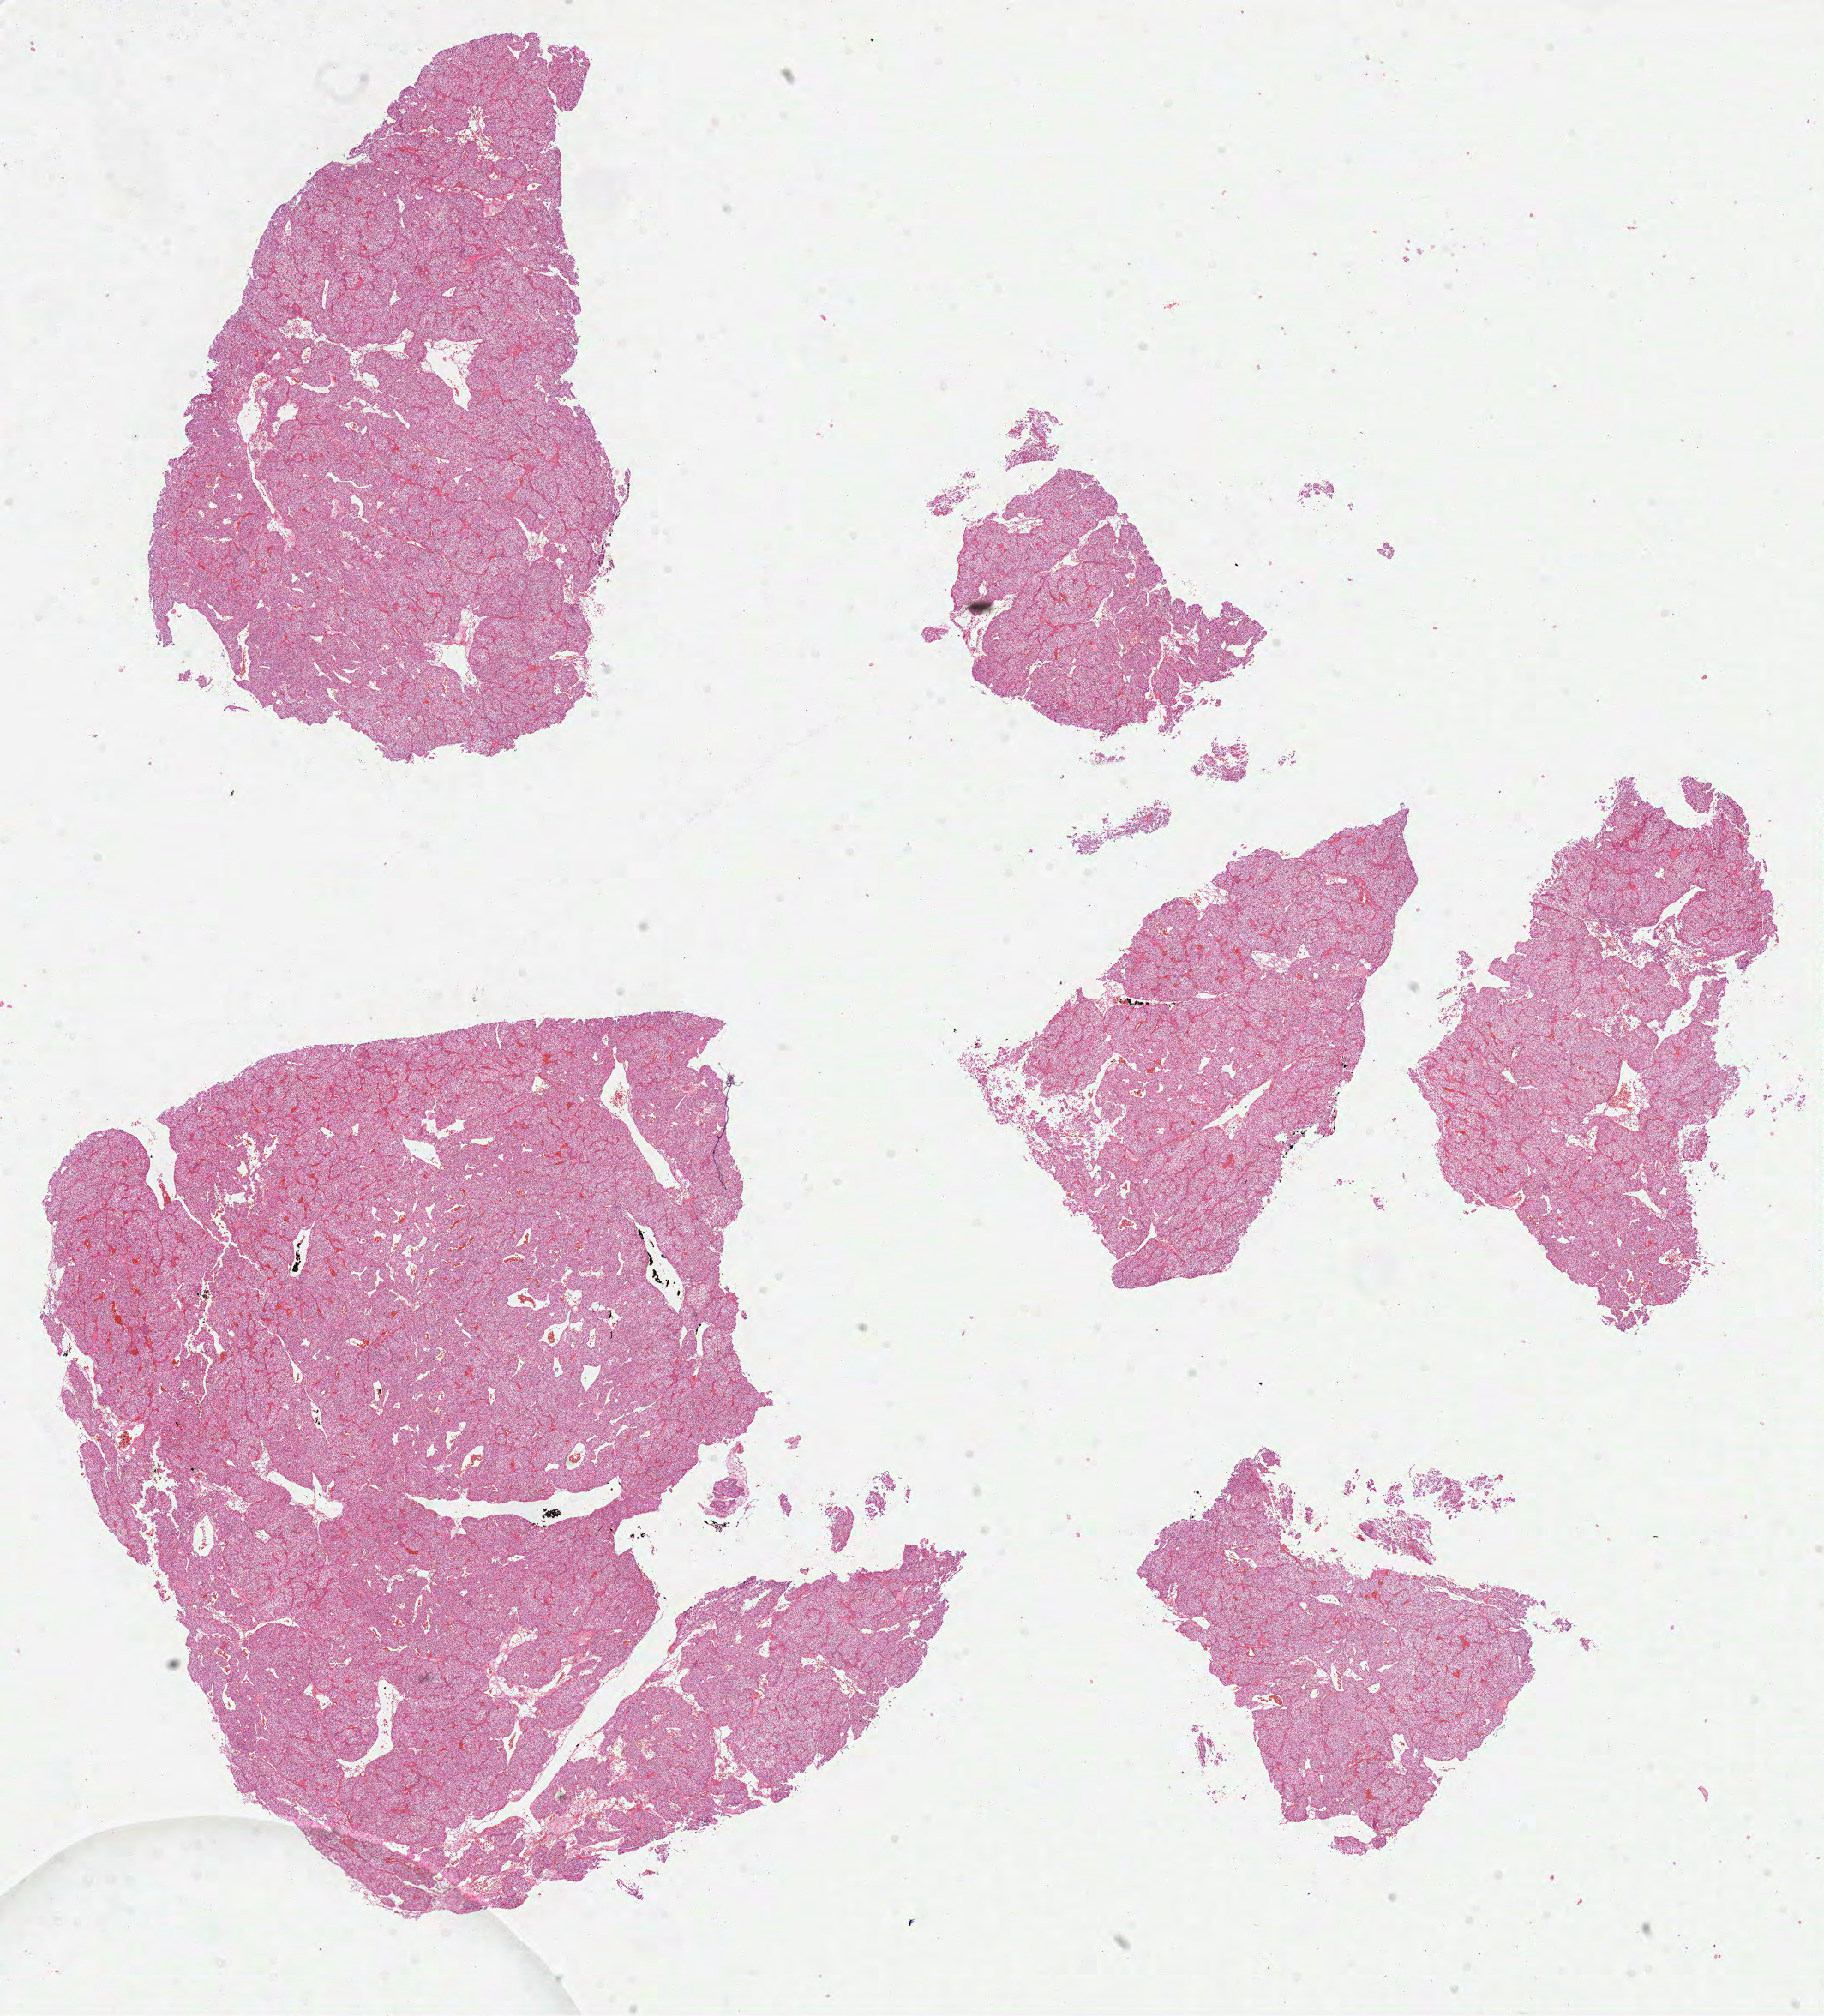
H&E-stained whole-slide image, shown as a low-resolution overview of the whole scanned area (about 17.2 x 19.0 mm); formalin-fixed paraffin-embedded (FFPE) diagnostic section; primary tumour sample from the kidney. Male patient; age at initial diagnosis 67 years. Histologic grade: G3 (poorly differentiated).
• AJCC pathologic stage: I
• diagnosis: Clear cell adenocarcinoma, NOS